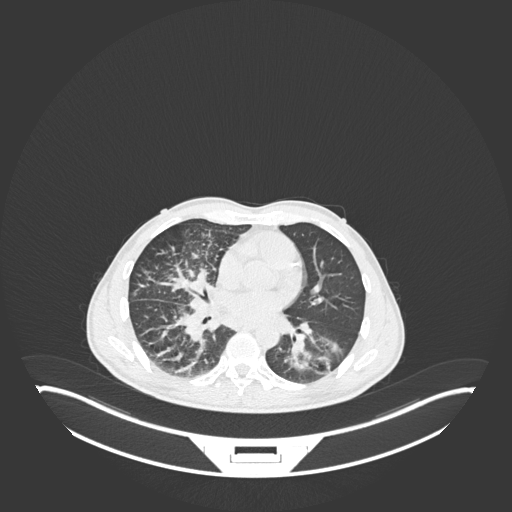
Chest CT, one axial slice. Slice 114 of 237 in the series (ordered by position). Reconstruction kernel B30f. 120 kVp. Lung window (W 1500 / L -600 HU). 1 mm slice thickness. 512 × 512 image matrix, field of view 500 × 500 mm. Male patient, age 49 years. Case-level facts recorded for this patient, not image findings: clinical TNM (as recorded): T2b N1 M0.
Outlined on this slice (bounding box drawn by a radiologist):
- lung tumour (recorded histology: adenocarcinoma): bounding box (x1, y1, x2, y2) in pixels: (284, 325, 348, 377)